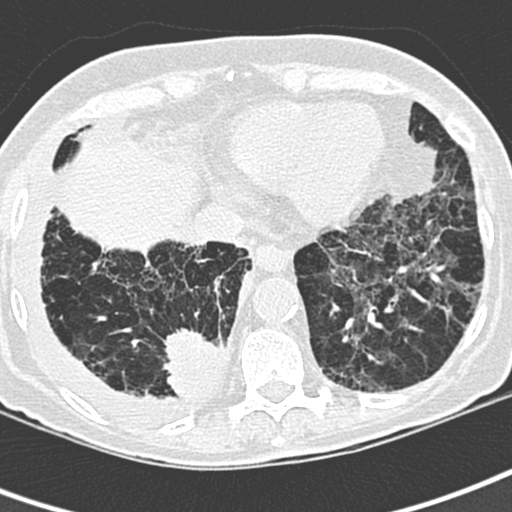
Low-dose screening chest CT, one axial slice; slice 76 of 220 in the series (ordered by position); 120 kVp; lung window (W 1500 / L -600 HU); 512 × 512 image matrix, field of view 288 × 288 mm.
Structures marked on this image (expert manual segmentation):
- lesion 1 (tumor, lower lobe of right lung): bounding box <164,329,222,398> (left, top, right, bottom; pixels)